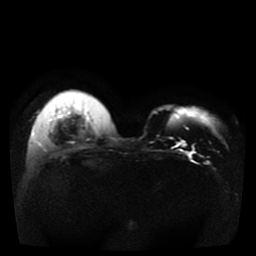
Breast MRI, one axial slice. Slice 10 of 41 in the series (ordered by position). Diffusion-weighted series; image 2 of 4 stored at this slice position (different b-values; order by instance number). 1.5 T. 5 mm slice thickness. 256 × 256 image matrix, field of view 330 × 330 mm. Female patient.
Outlined on this slice (outlined manually by an expert reader):
- tumour on diffusion-weighted imaging: bounding box [x1, y1, x2, y2] px = [179, 141, 186, 147]